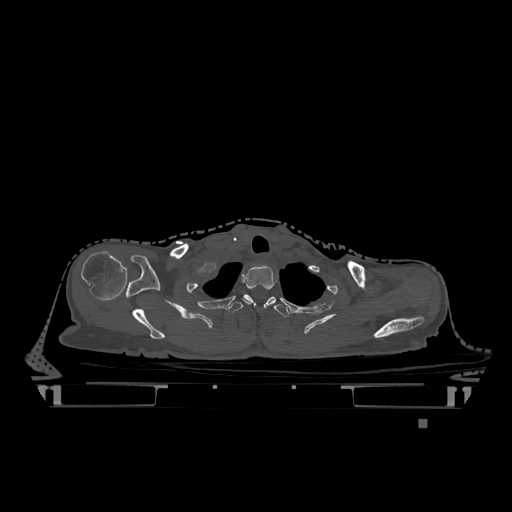
CT including the spine, one axial slice. Position 983 of 1317 along the scan axis. Bone window (W 1800 / L 400 HU). 512 × 512 image matrix. Patient: female, 74 years. From the clinical record (not read from this slice): primary cancer: lung.
Outlined on this slice (semi-automatically segmented with operator editing):
- T1 vertebra: box from (x=243, y=265) to (x=275, y=305) px
- T2 vertebra: (x=227, y=294)–(x=290, y=318)